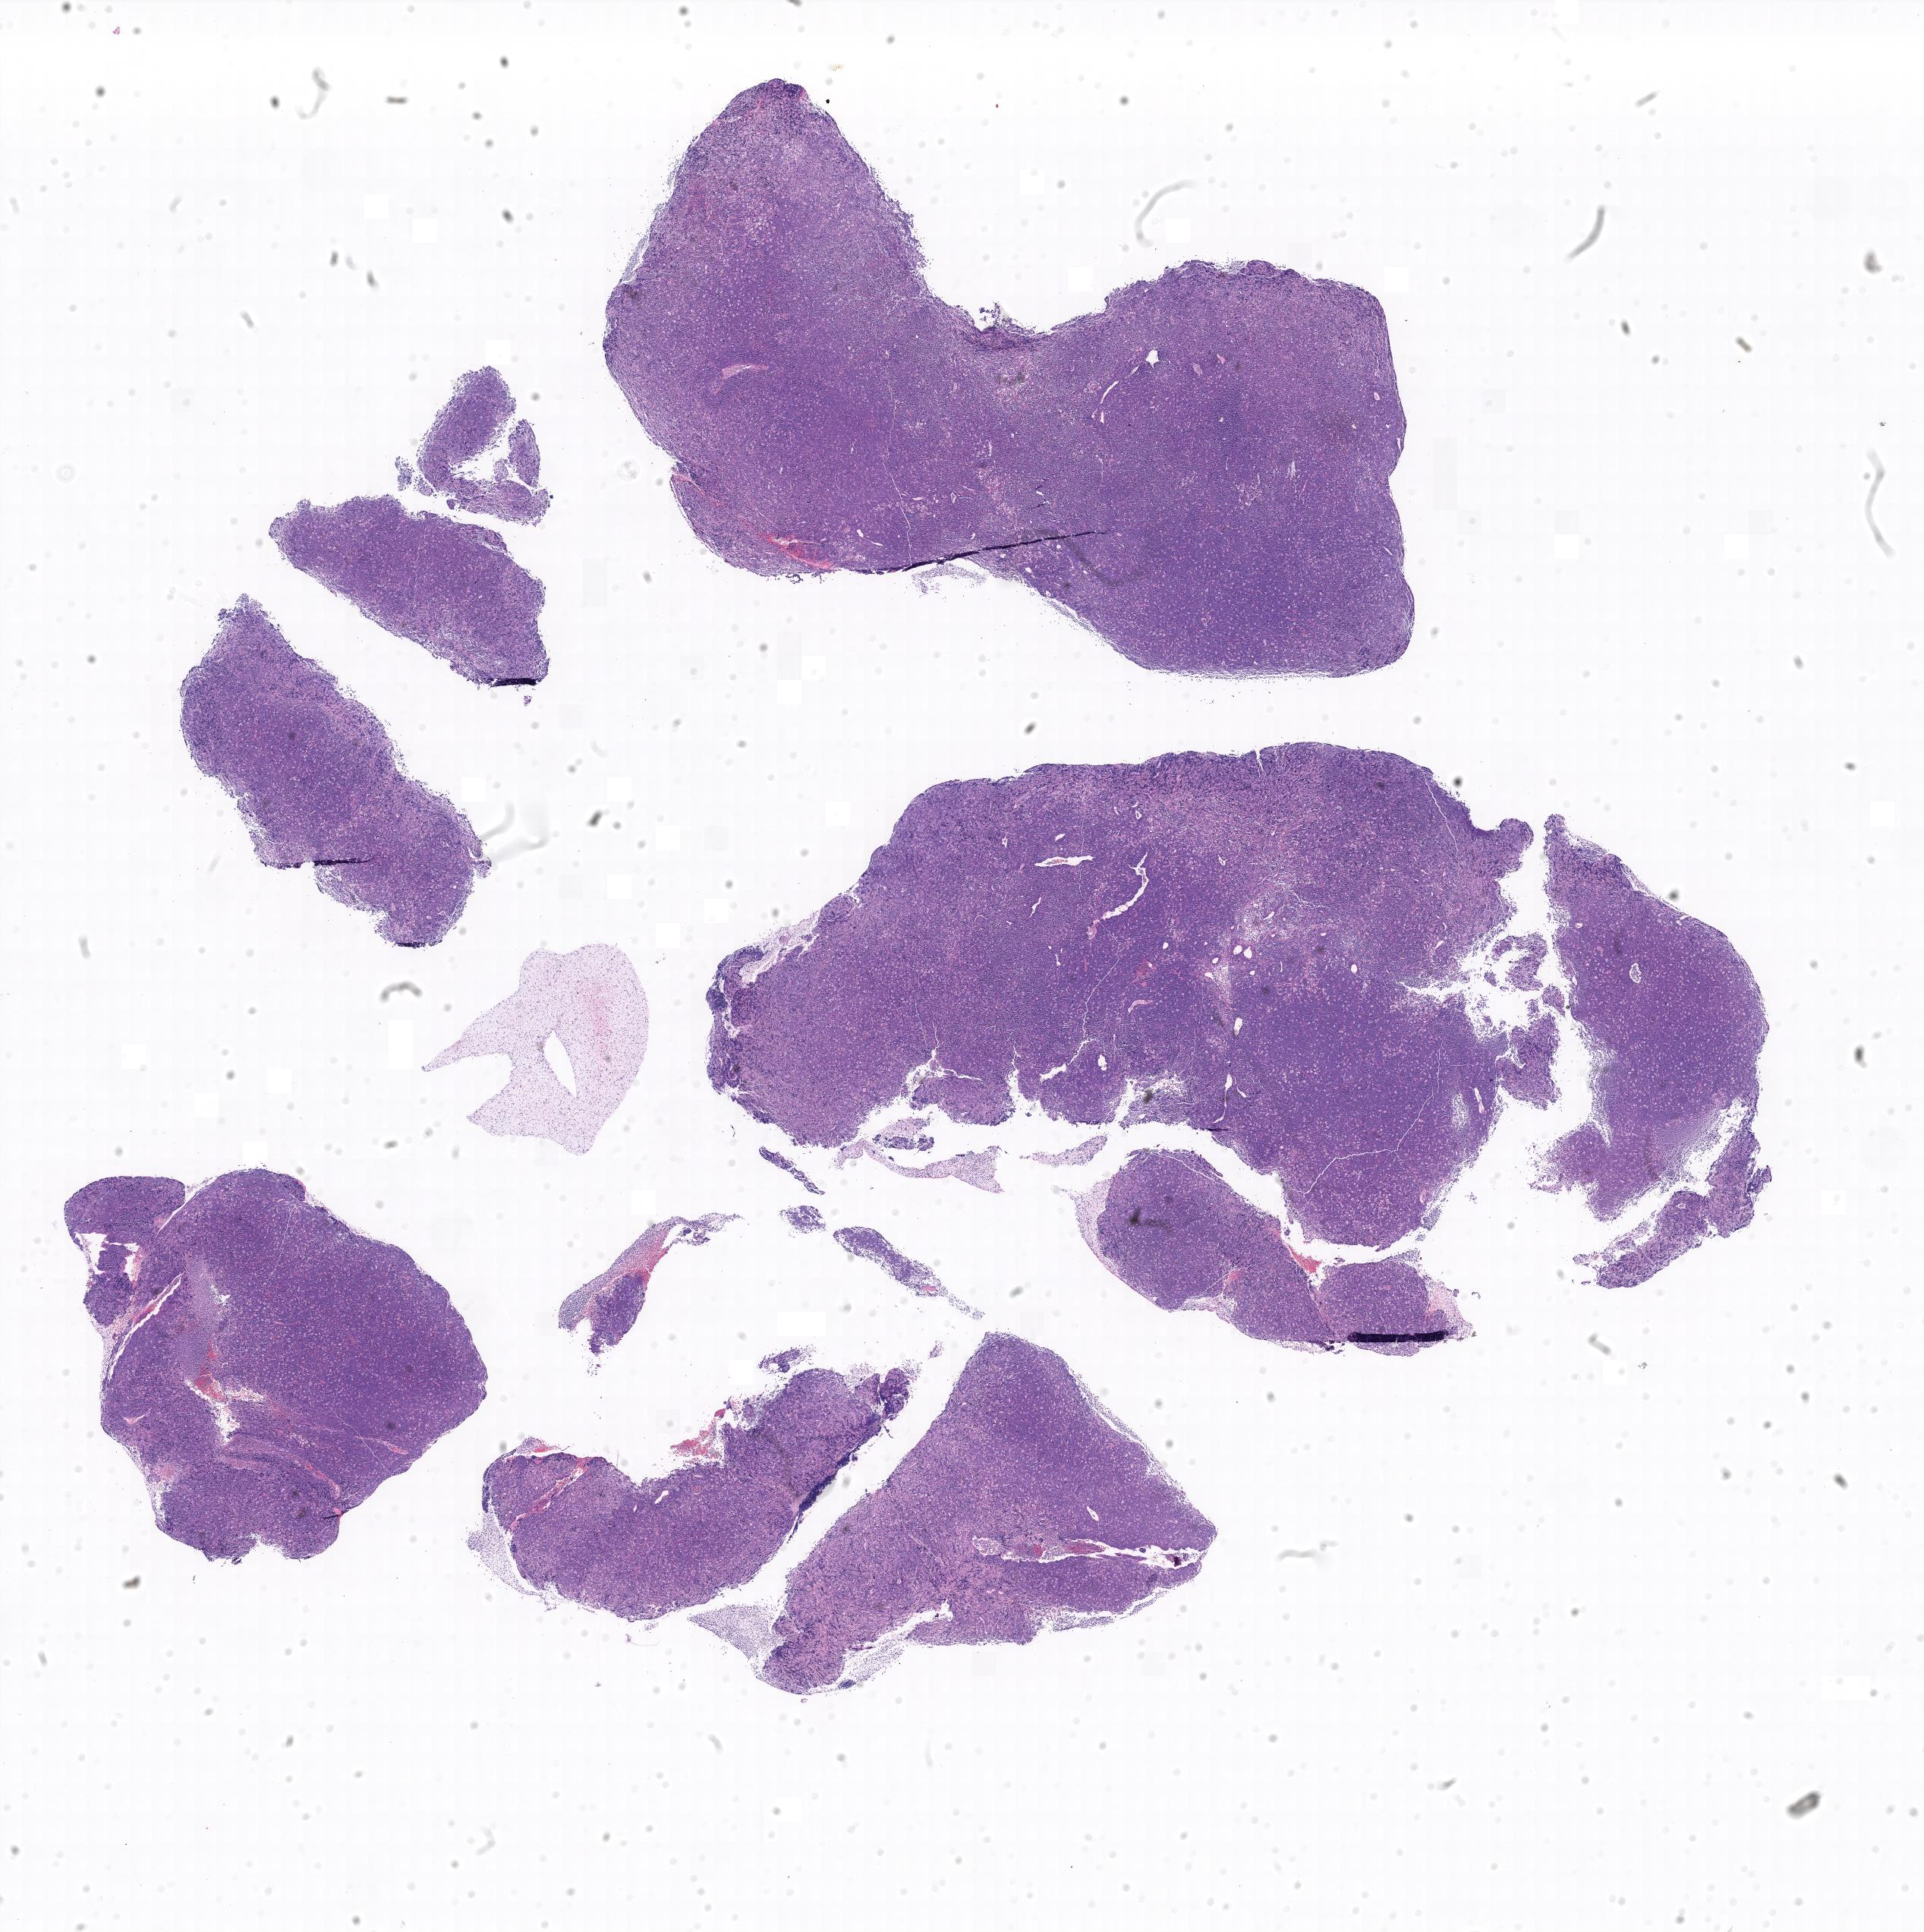
Whole-slide image, H&E stain — shown as a low-resolution overview of the whole scanned area. Specimen: tumor tissue. Anatomic site: soft tissue. Patient: female, age at initial diagnosis 9 years.
Diagnosis: Burkitt lymphoma, NOS.